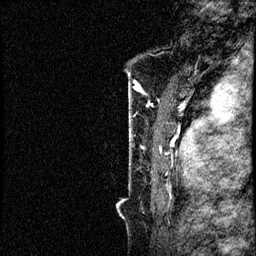
Breast MRI (dynamic contrast-enhanced), one sagittal slice. Position 8 of 60 along the scan axis. Dynamic contrast-enhanced study with each time point stored as its own series, time point 2 of 4 at this slice position (early post-contrast, ordered by acquisition time). 1.5 T. TE 4.2 ms, TR 17.6 ms. 2 mm slice thickness. 256 × 256 image matrix, field of view 200 × 200 mm. Female patient, age 40 years. From the clinical record (not read from this slice): setting: breast cancer imaged before/during neoadjuvant chemotherapy; receptor status: HER2-positive.
Annotated regions visible in this slice (semi-automatically segmented with operator editing):
- analysis volume of interest (the breast-tissue region the enhancement analysis was run in; not a lesion): bounding box <118,56,197,205> (left, top, right, bottom; pixels)
- tumour enhancement mask (voxels above the 100 % enhancement threshold inside the analysis volume of interest): <142,92,197,197>